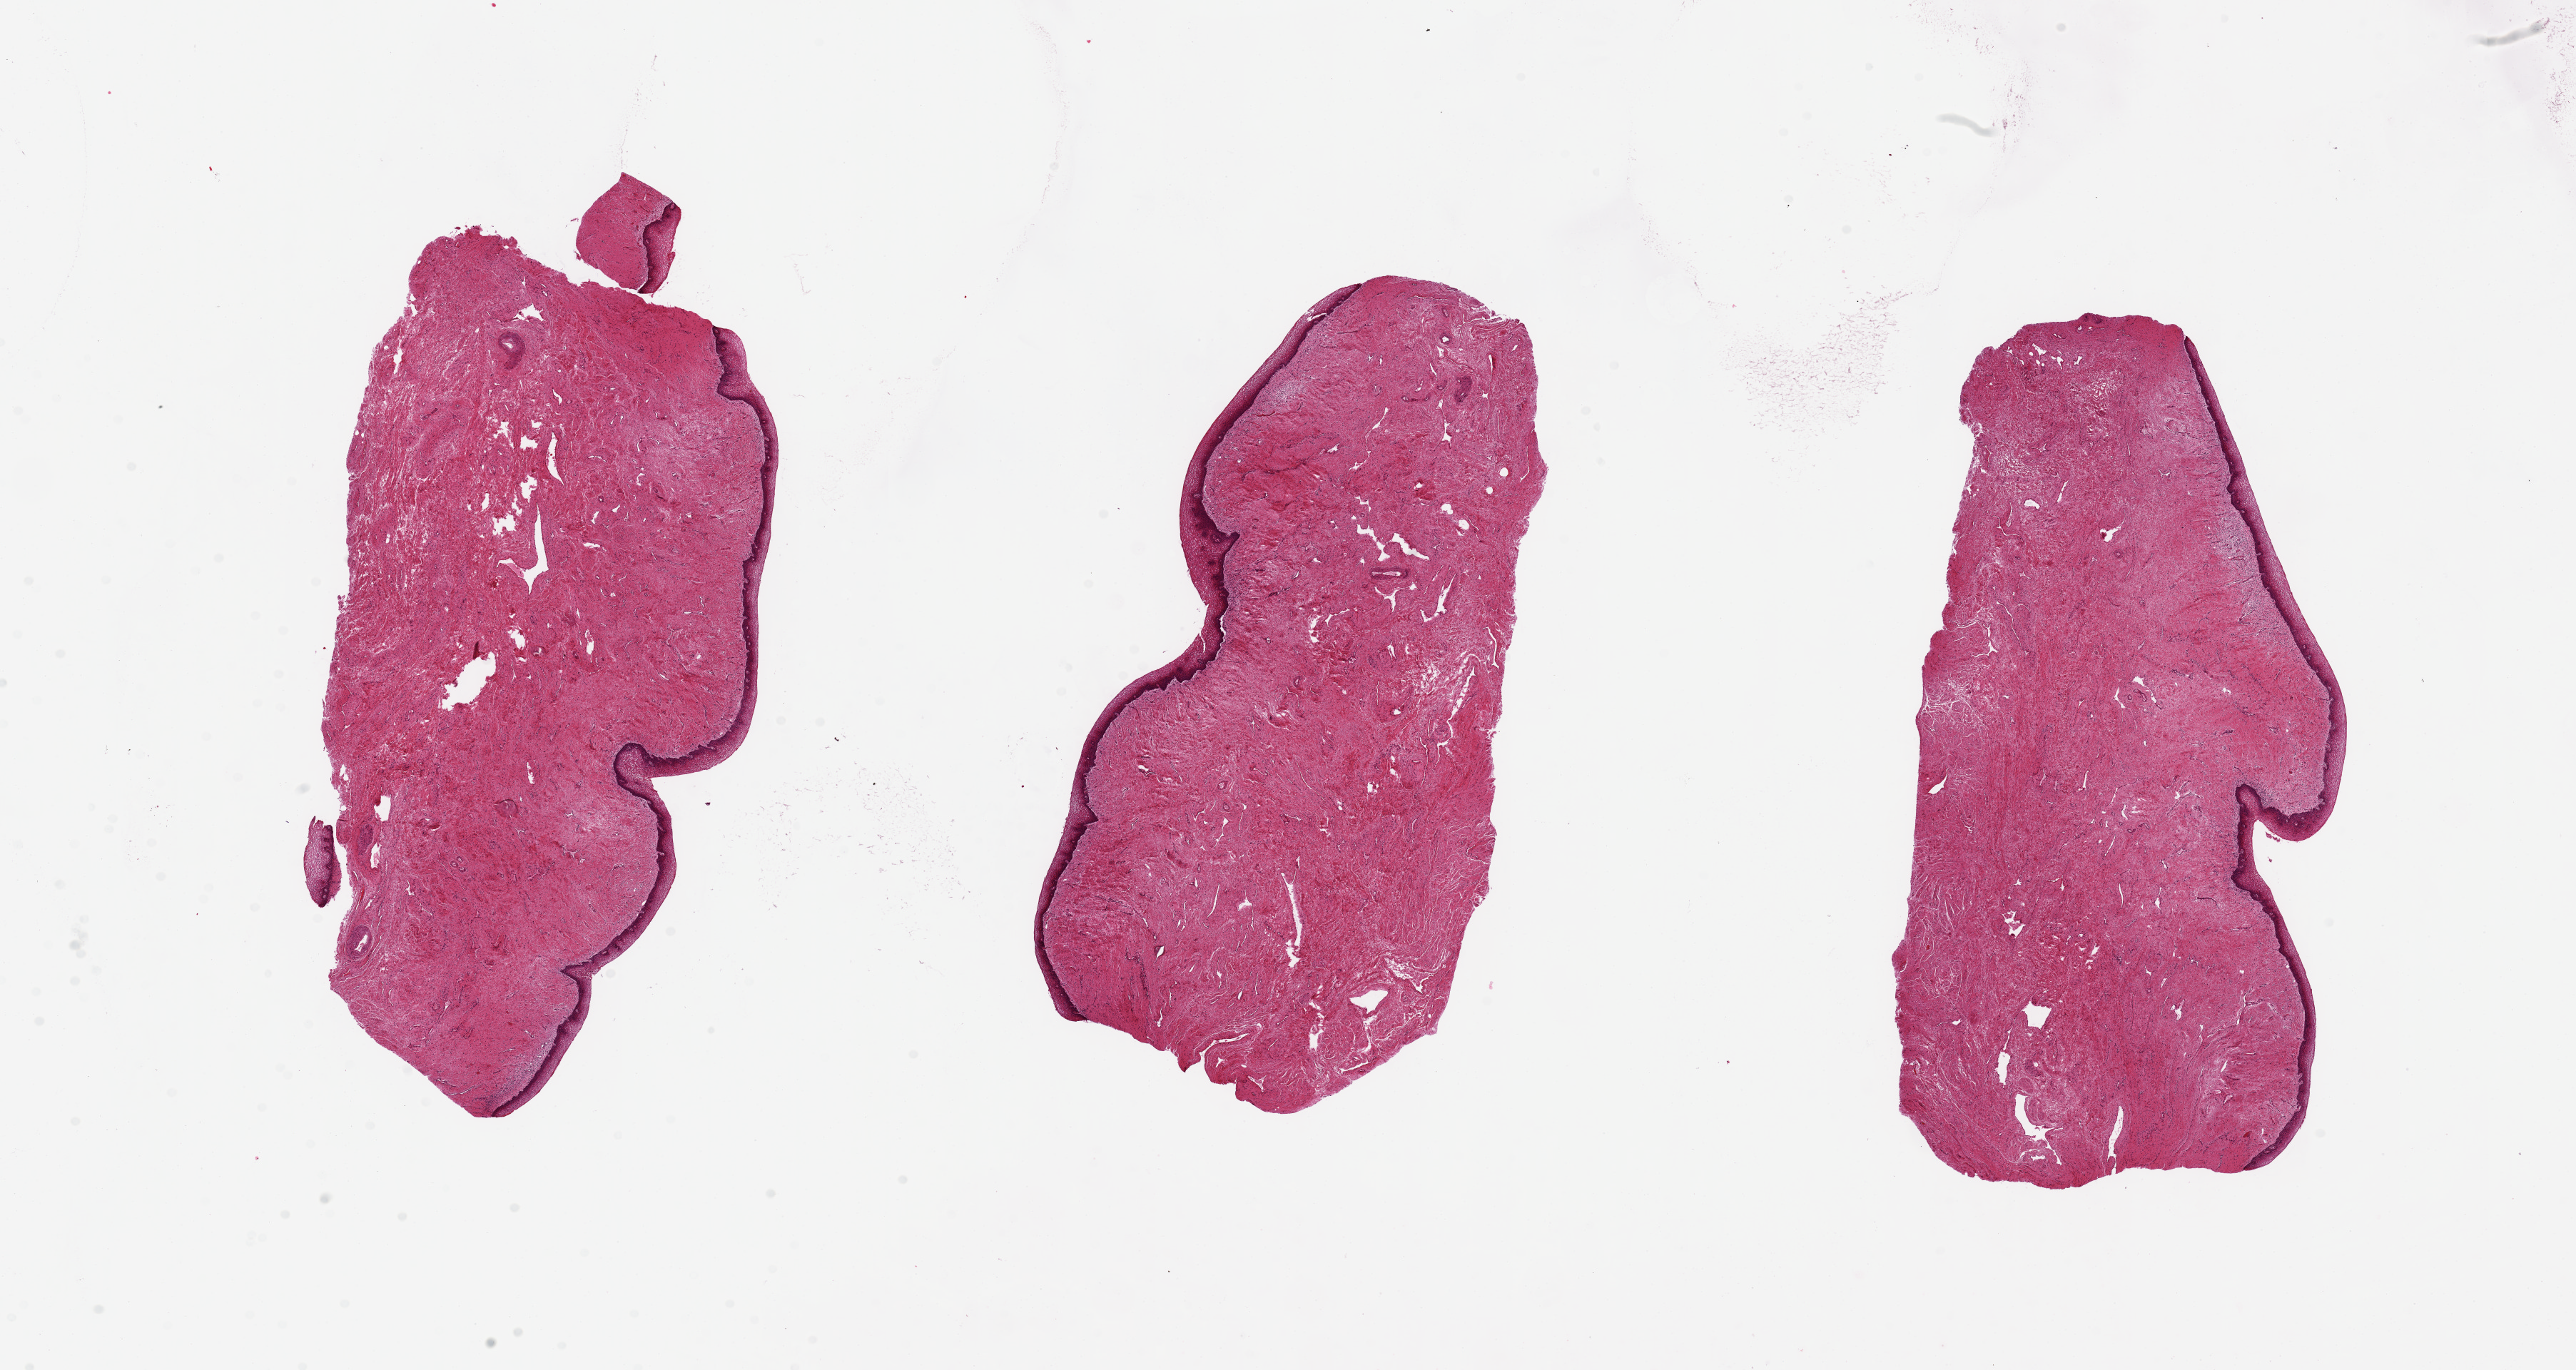
Haematoxylin and eosin whole-slide image — whole scanned area (about 28.5 x 15.2 mm) shown as a low-resolution overview; PAXgene-fixed paraffin-embedded (PFPE) section; sampled site (target tissue): vagina; donor tissue sample. Female donor.
- review note (as recorded): 3 pieces, 9x4.8 mm